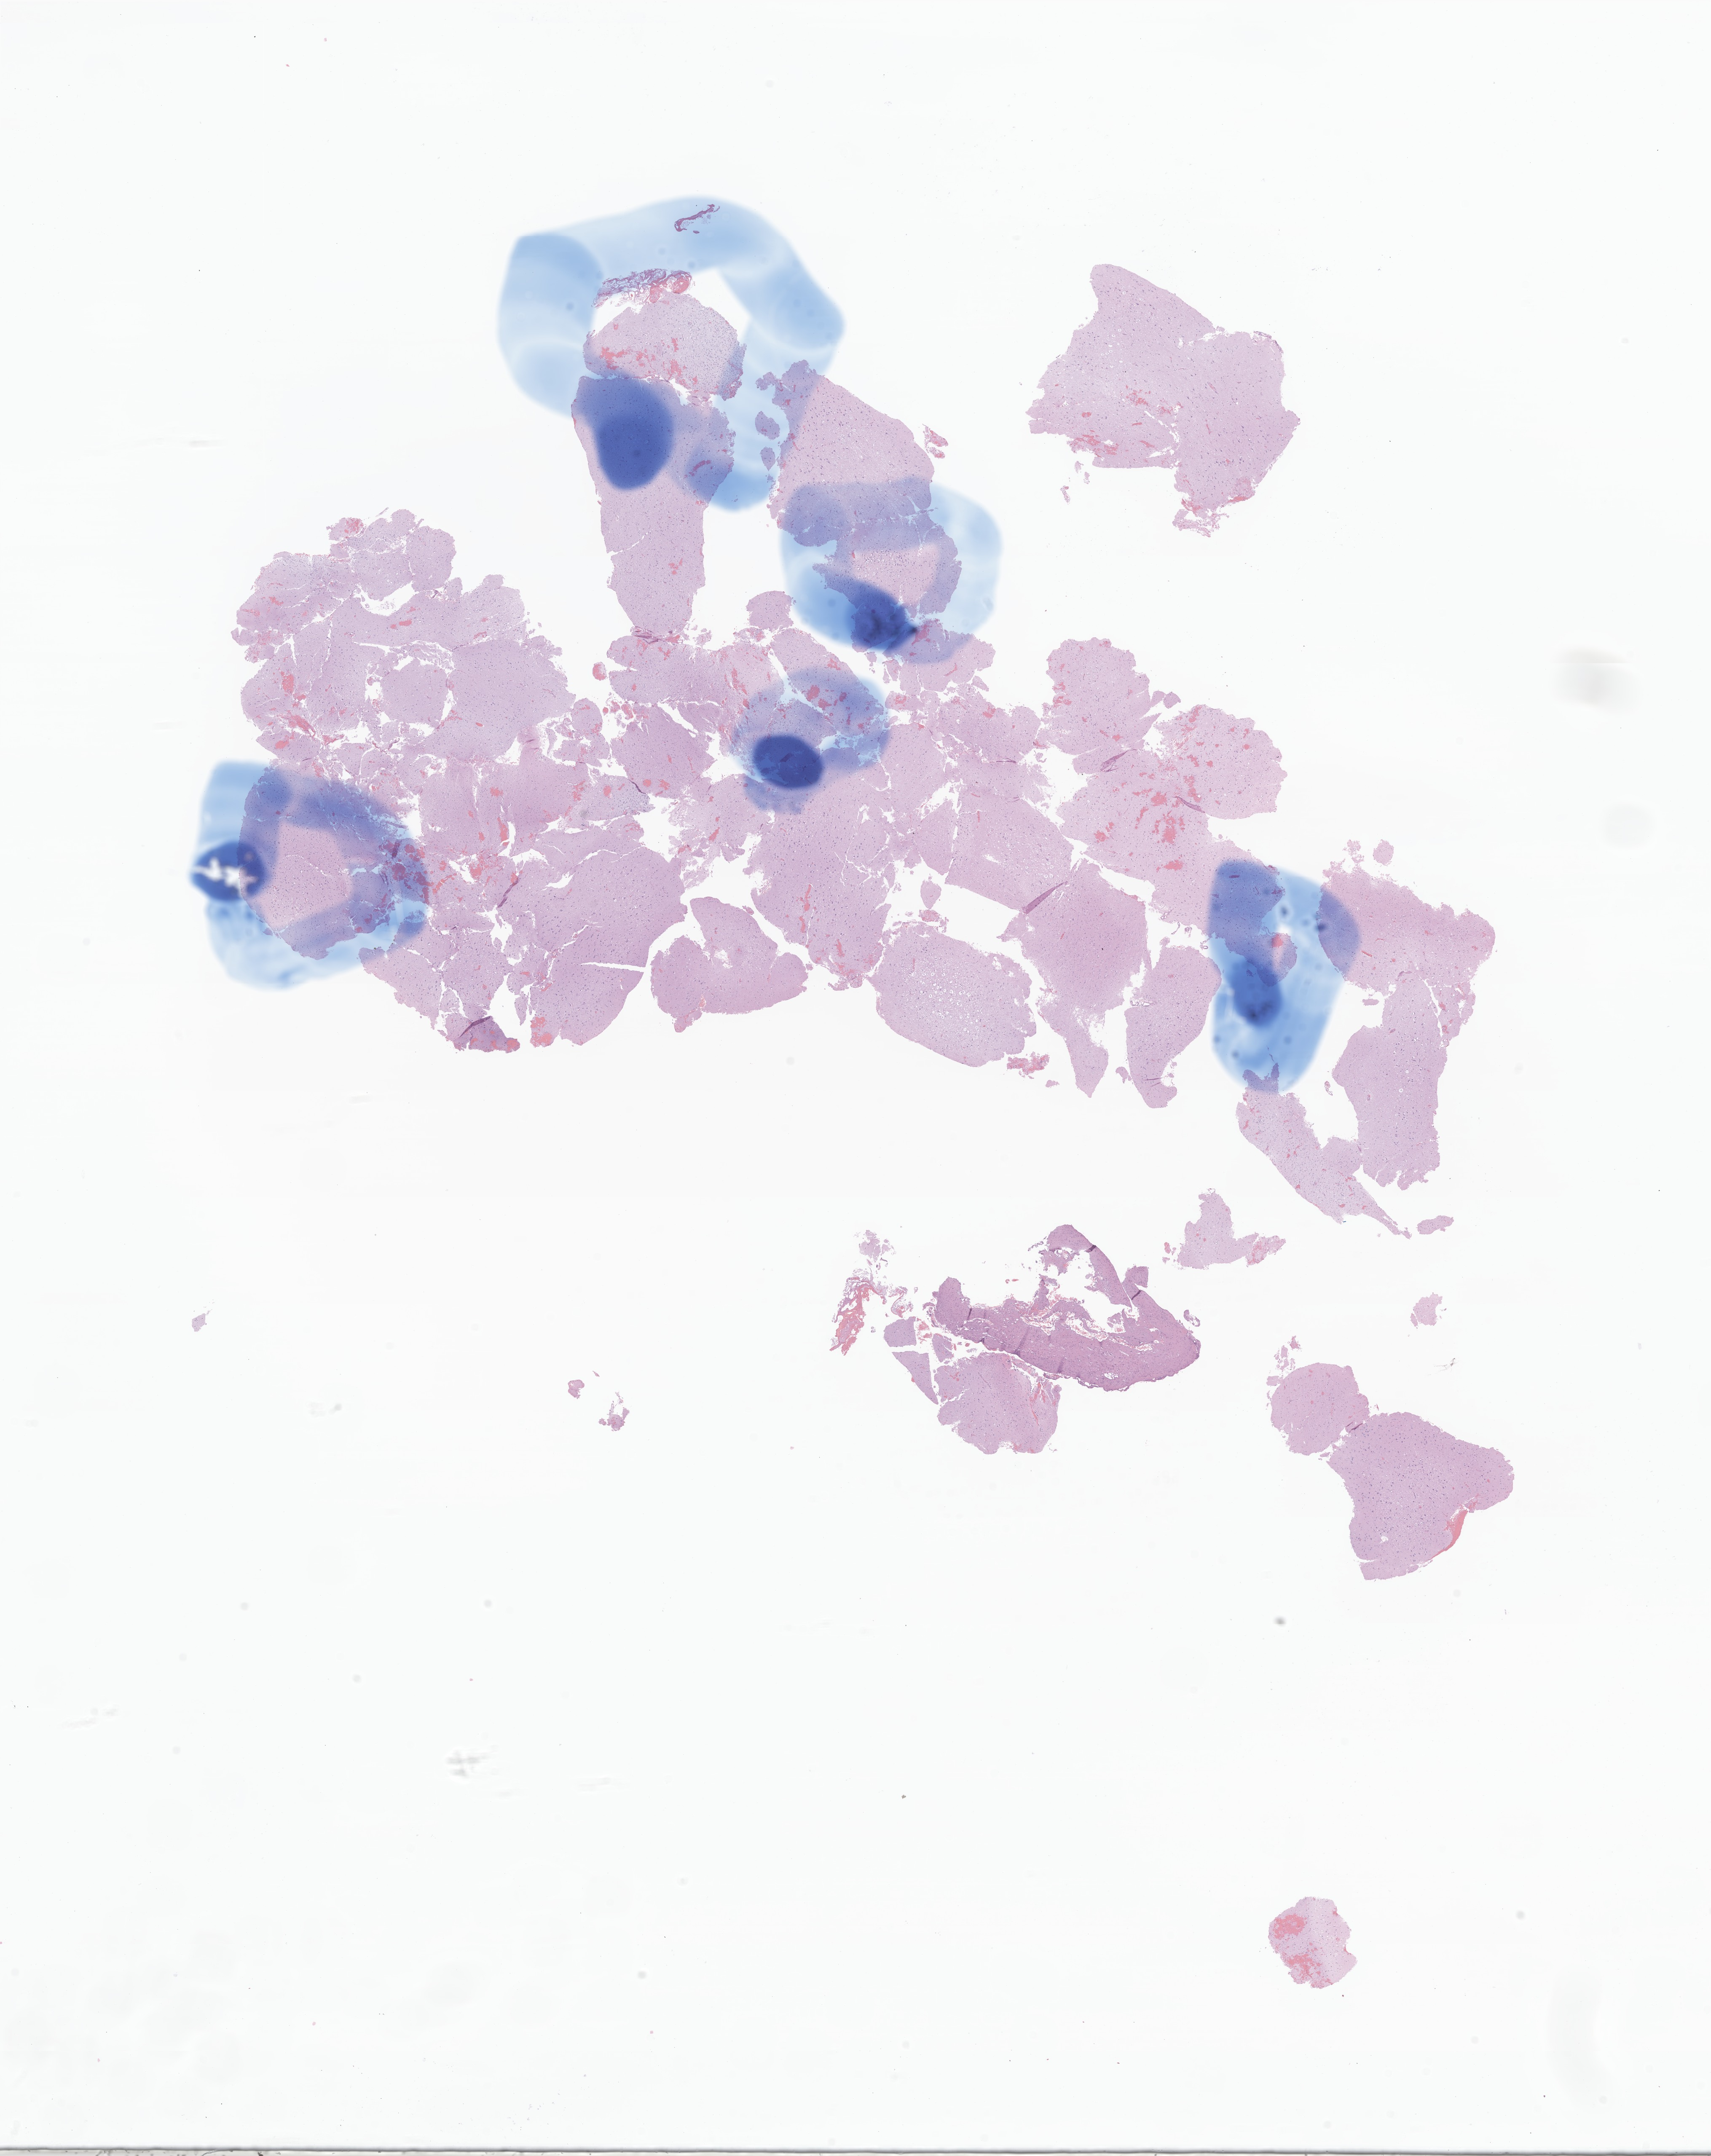
Whole-slide image, H&E stain of tumor tissue from the brain, whole scanned area (about 17.1 x 21.6 mm) shown as a low-resolution overview, FFPE section. Patient: male, age 173 months (14 years 5 months).
* recorded diagnosis: Glioma, malignant